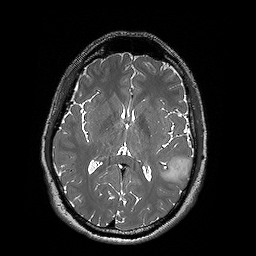
Brain MRI from a brain-tumour surgery series, one axial slice; slice 86 of 192 in the series (ordered by position); 1 mm slice thickness; 256 × 256 image matrix, field of view 250 × 250 mm. From the clinical record (not read from this slice): histopathology: Oligodendroglioma; WHO grade: 2; IDH mutation: yes; tumour location: Left Posterior Temporal.
Outlined on this slice (manually delineated by an expert):
- tumour: bounding box [x1, y1, x2, y2] px = [159, 156, 193, 180]